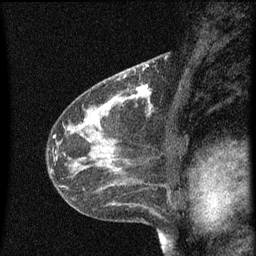
Breast MRI (dynamic contrast-enhanced), one sagittal slice; slice 32 of 60 in the series (ordered by position); dynamic contrast-enhanced series, image 2 of 3 at this slice position (ordered by acquisition); 1.5 T; TE 4.2 ms, TR 8 ms; 256 × 256 image matrix. Patient: female, 41 years.
Structures marked on this image (semi-automatically segmented with operator editing):
- analysis volume of interest (the breast-tissue region the enhancement analysis was run in; not a lesion): bounding box [x1, y1, x2, y2] px = [130, 76, 153, 103]
- tumour enhancement mask (voxels above the 70 % enhancement threshold inside the analysis volume of interest): [130, 84, 153, 103]